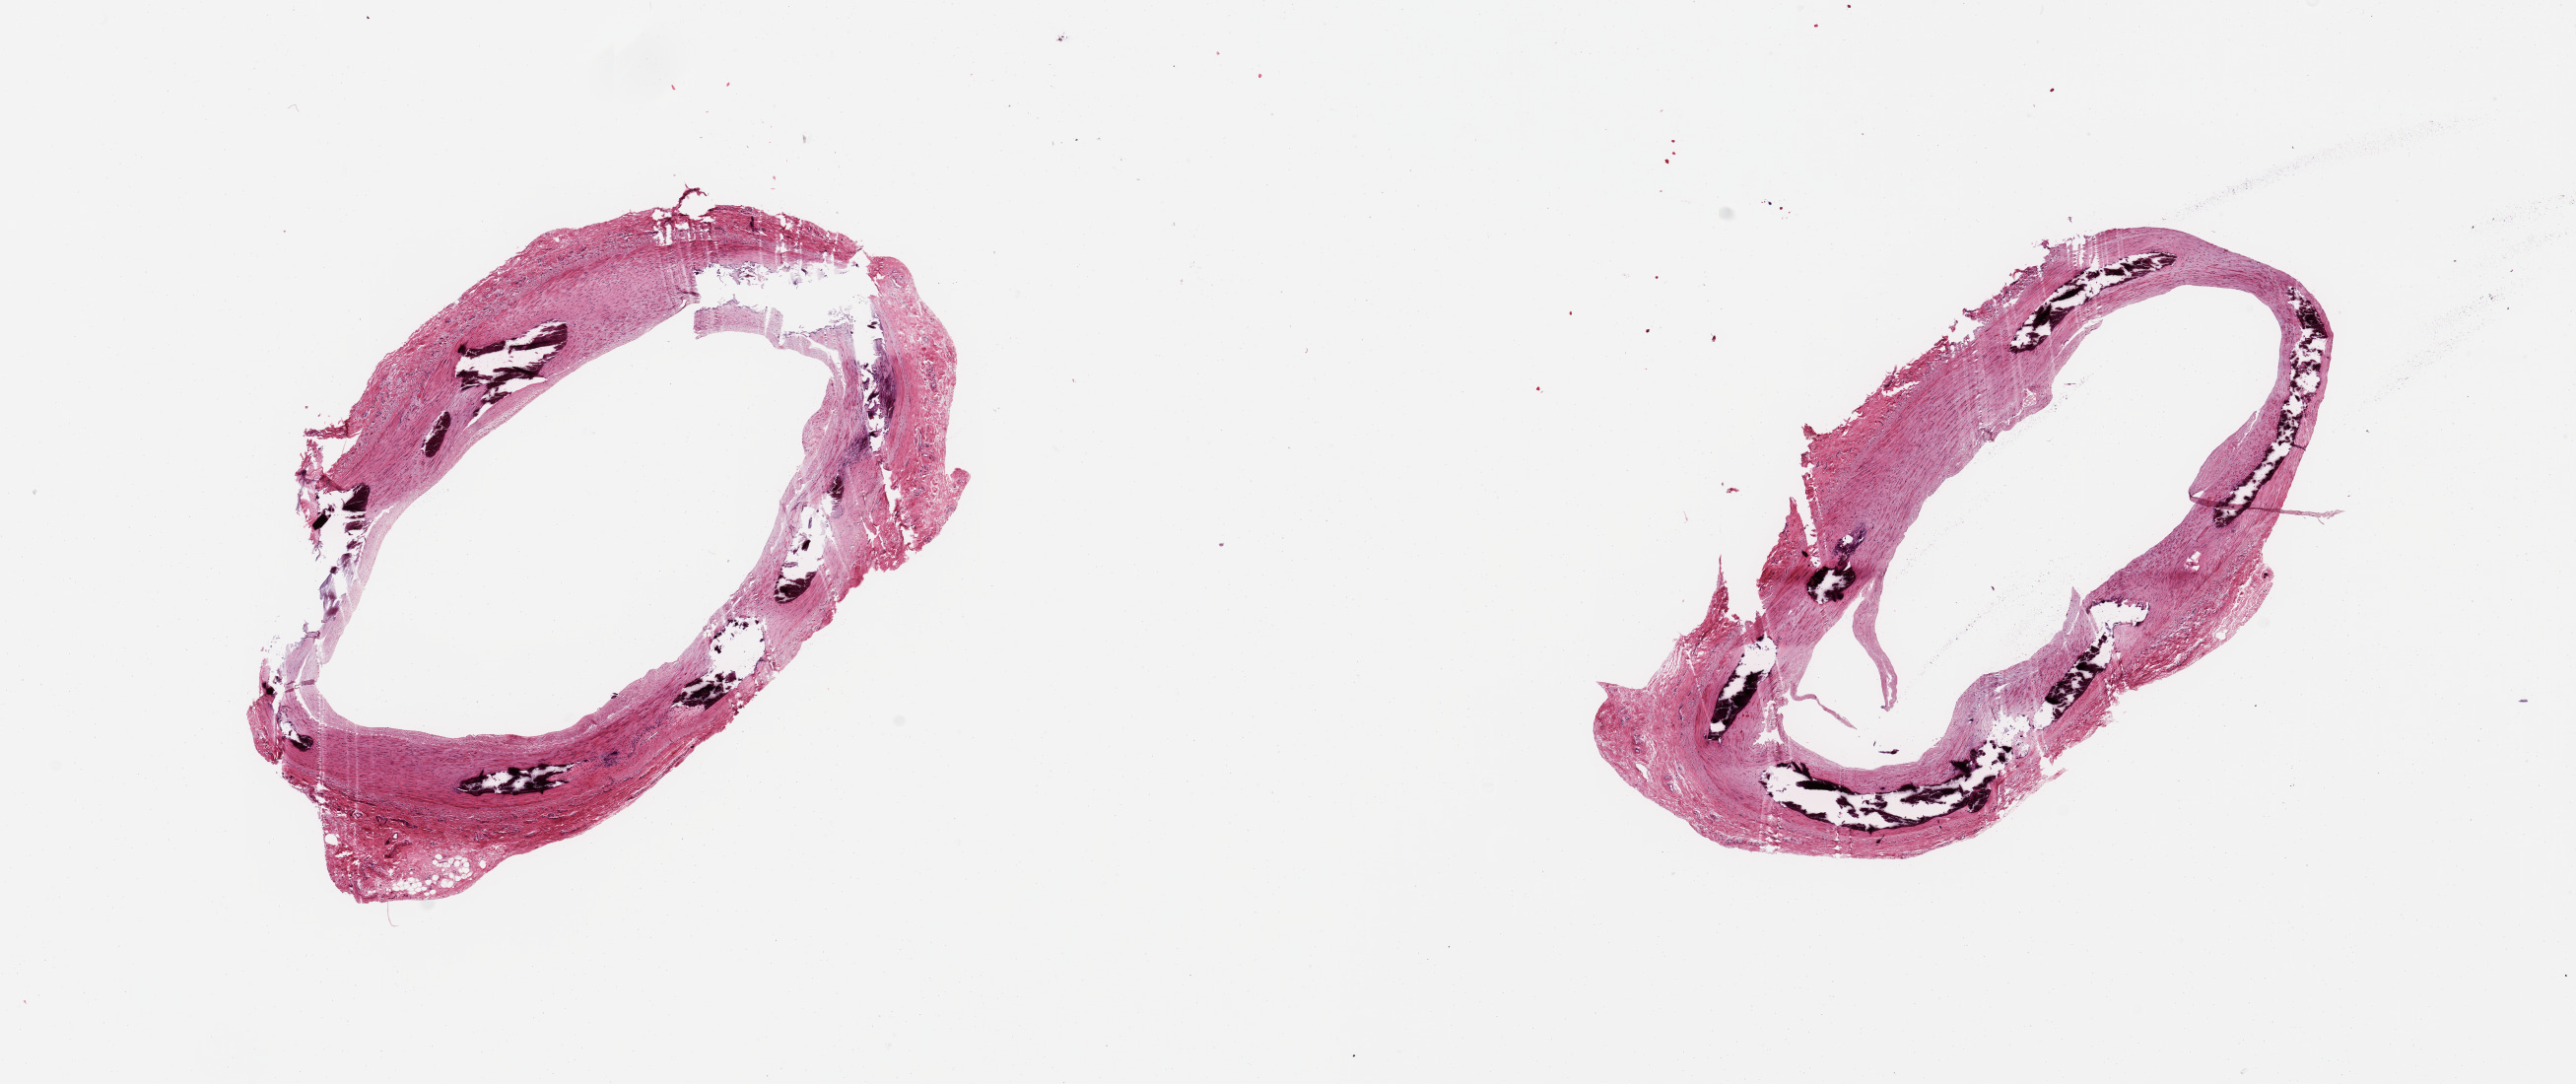
Digitized haematoxylin and eosin-stained section, brightfield — whole scanned area (about 20.7 x 8.7 mm) shown as a low-resolution overview; PAXgene-fixed paraffin-embedded (PFPE) section; target tissue: tibial artery; donor tissue sample. Donor: female.
Review note (as recorded): 2 pieces, small muscular artery, Monckeberg sclerosis; focal atherosis.